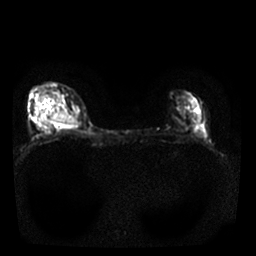
Breast MRI, one axial slice; slice 12 of 25 in the series (ordered by position); diffusion-weighted series; image 2 of 4 stored at this slice position (different b-values; order by instance number); 1.5 T; 256 × 256 image matrix, field of view 310 × 310 mm. Female patient.
Structures marked on this image (expert manual segmentation):
- tumour on diffusion-weighted imaging: box from (x=56, y=116) to (x=78, y=125) px